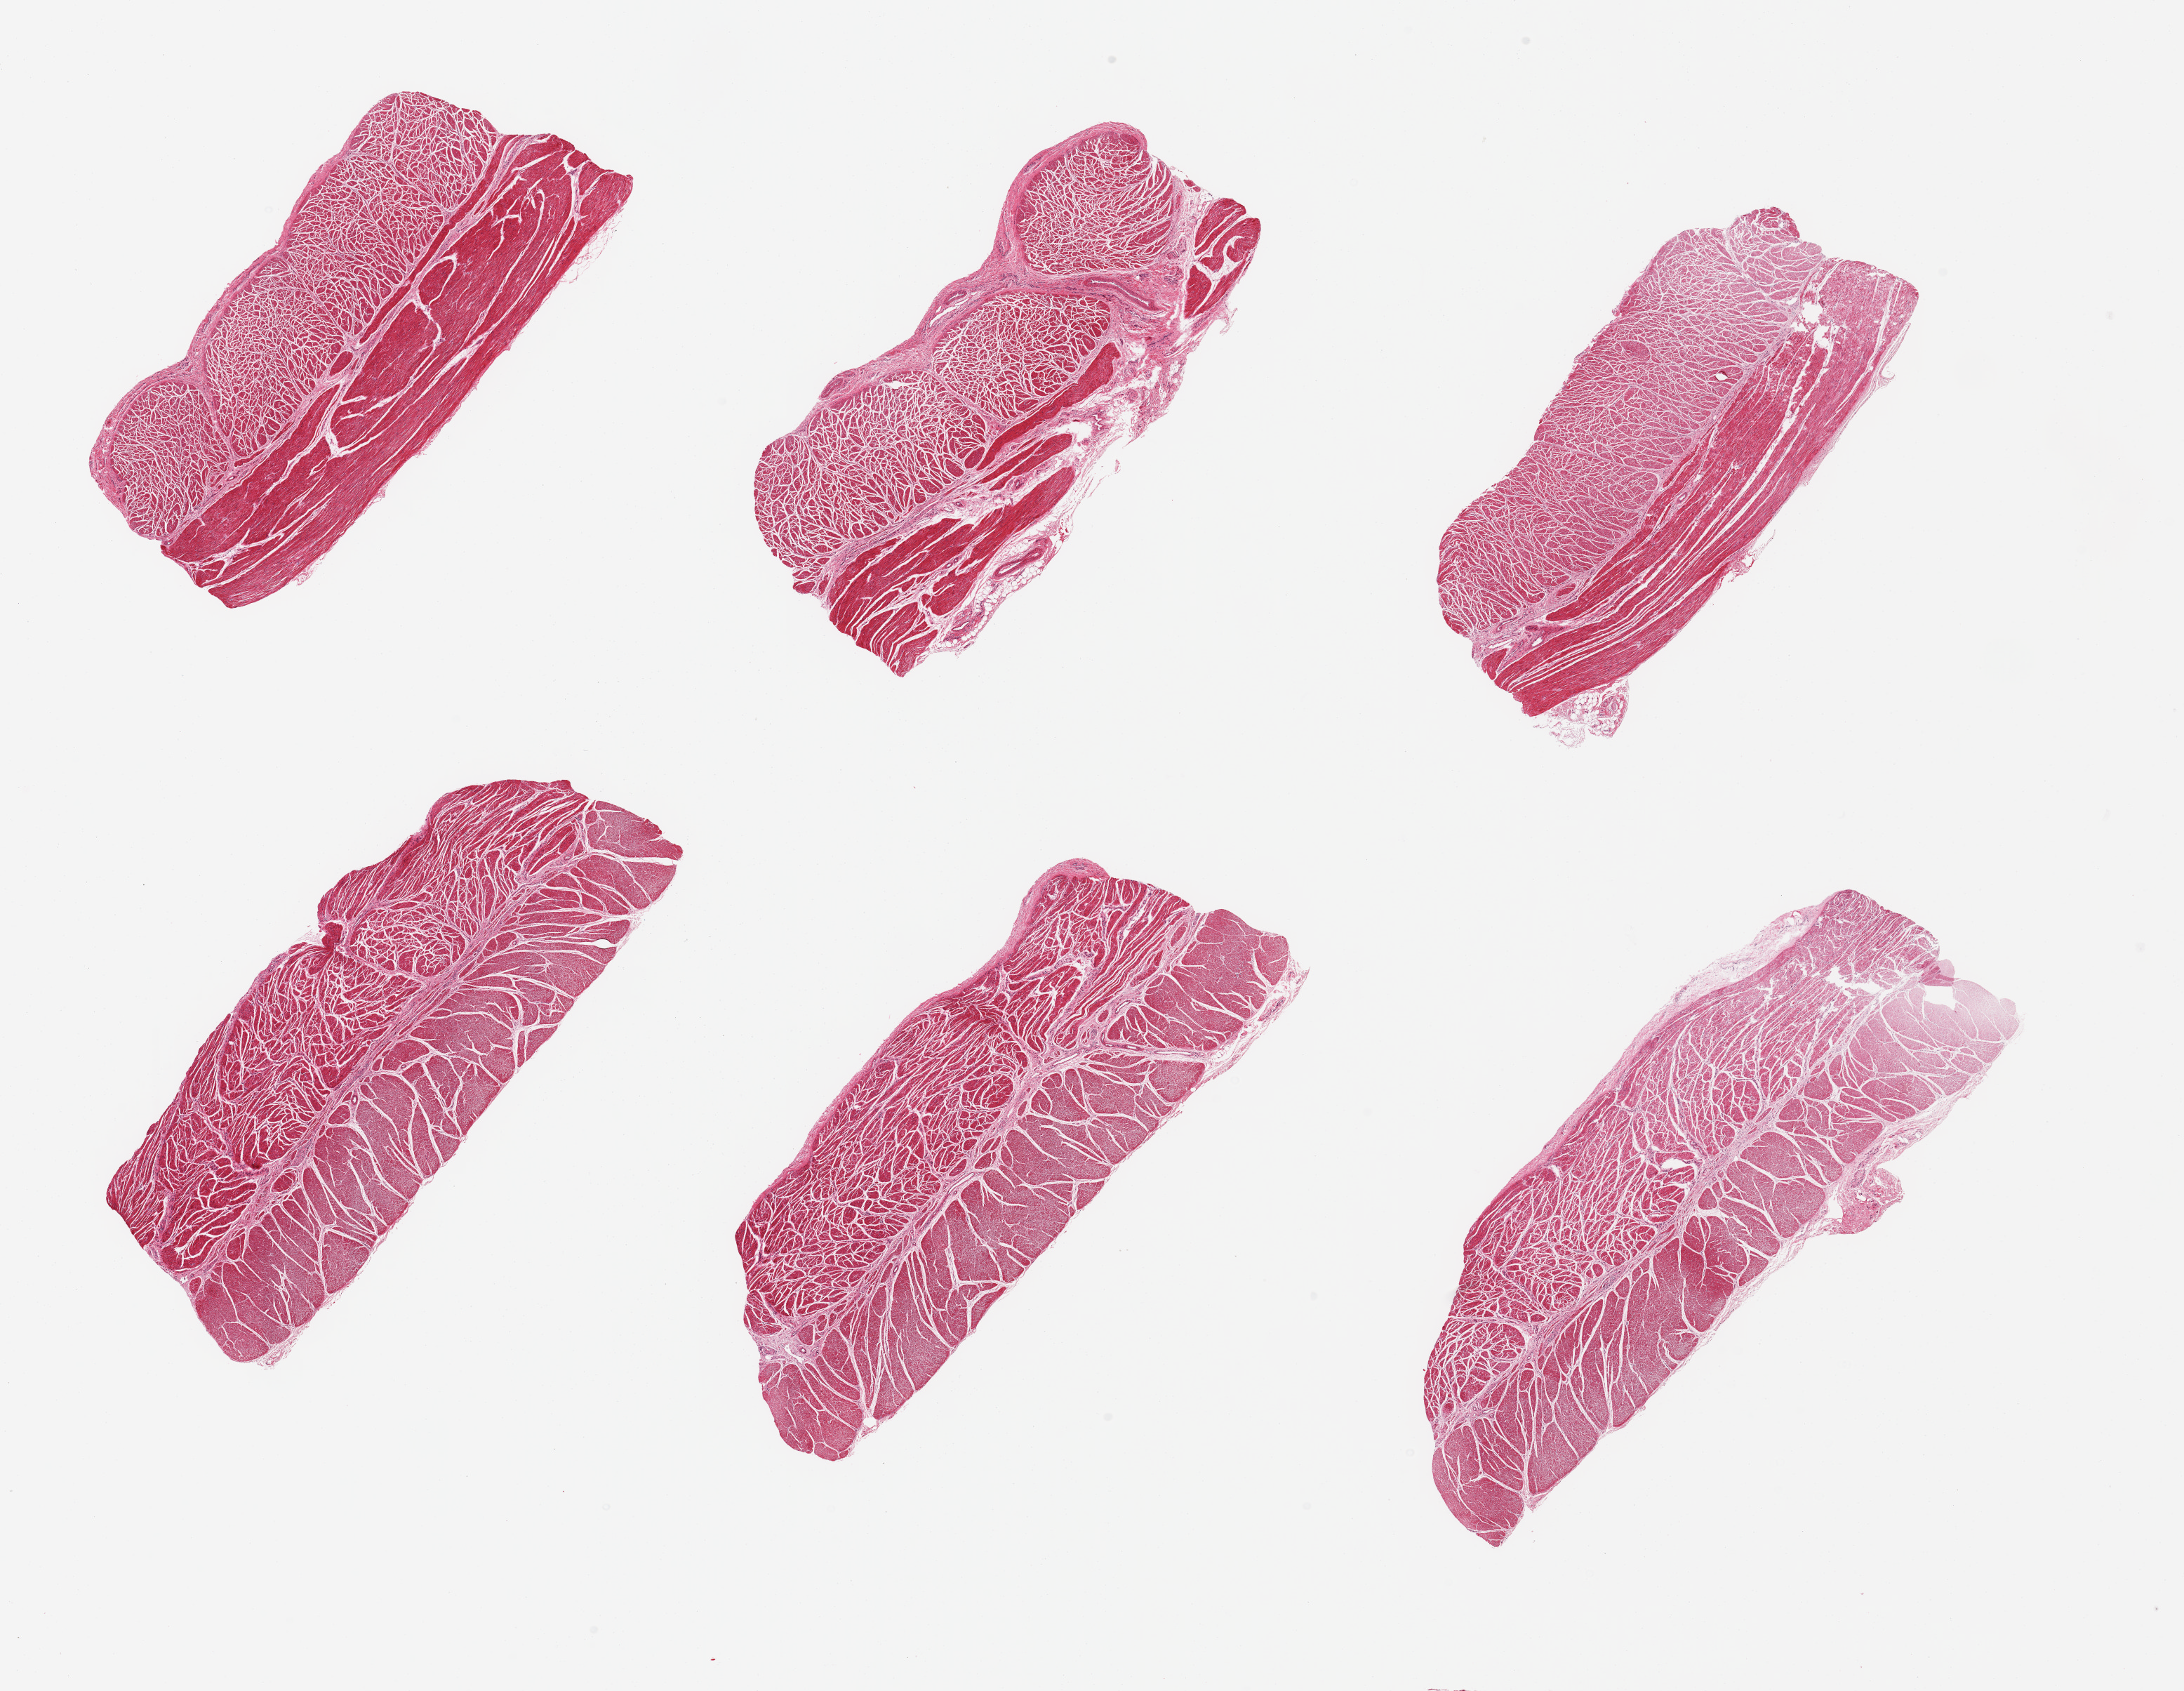
Digitized hematoxylin and eosin (H&E)-stained section — whole scanned area (about 24.6 x 19.1 mm, acquisition: 20x scan) shown as a low-resolution overview. PAXgene-fixed, paraffin-embedded tissue. Section of gastroesophageal junction (target tissue). Tissue donor sample. Donor sex: male.
Review note (as recorded): 6 pieces; well dissected.